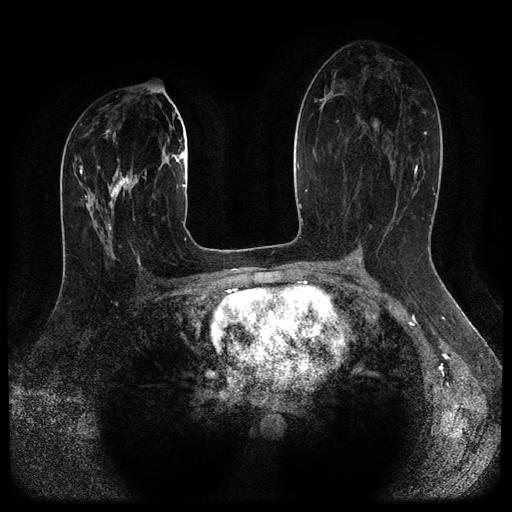
Breast MRI (dynamic contrast-enhanced, multi-phase), one axial slice; slice 55 of 116 in the series (ordered by position); dynamic contrast-enhanced series, time point 2 of 5 at this slice position (early post-contrast); 1.5 T; TE 2.6 ms, TR 5.4 ms; 2 mm slice thickness; 512 × 512 image matrix. Patient: female, 29 years.
Outlined on this slice (semi-automatic segmentation, software-assisted and operator-edited):
- breast lesion (labelled 'tumour' in the annotation; benign lesions carry a separate 'benign' label): bounding box (x1, y1, x2, y2) in pixels: (107, 168, 138, 203)